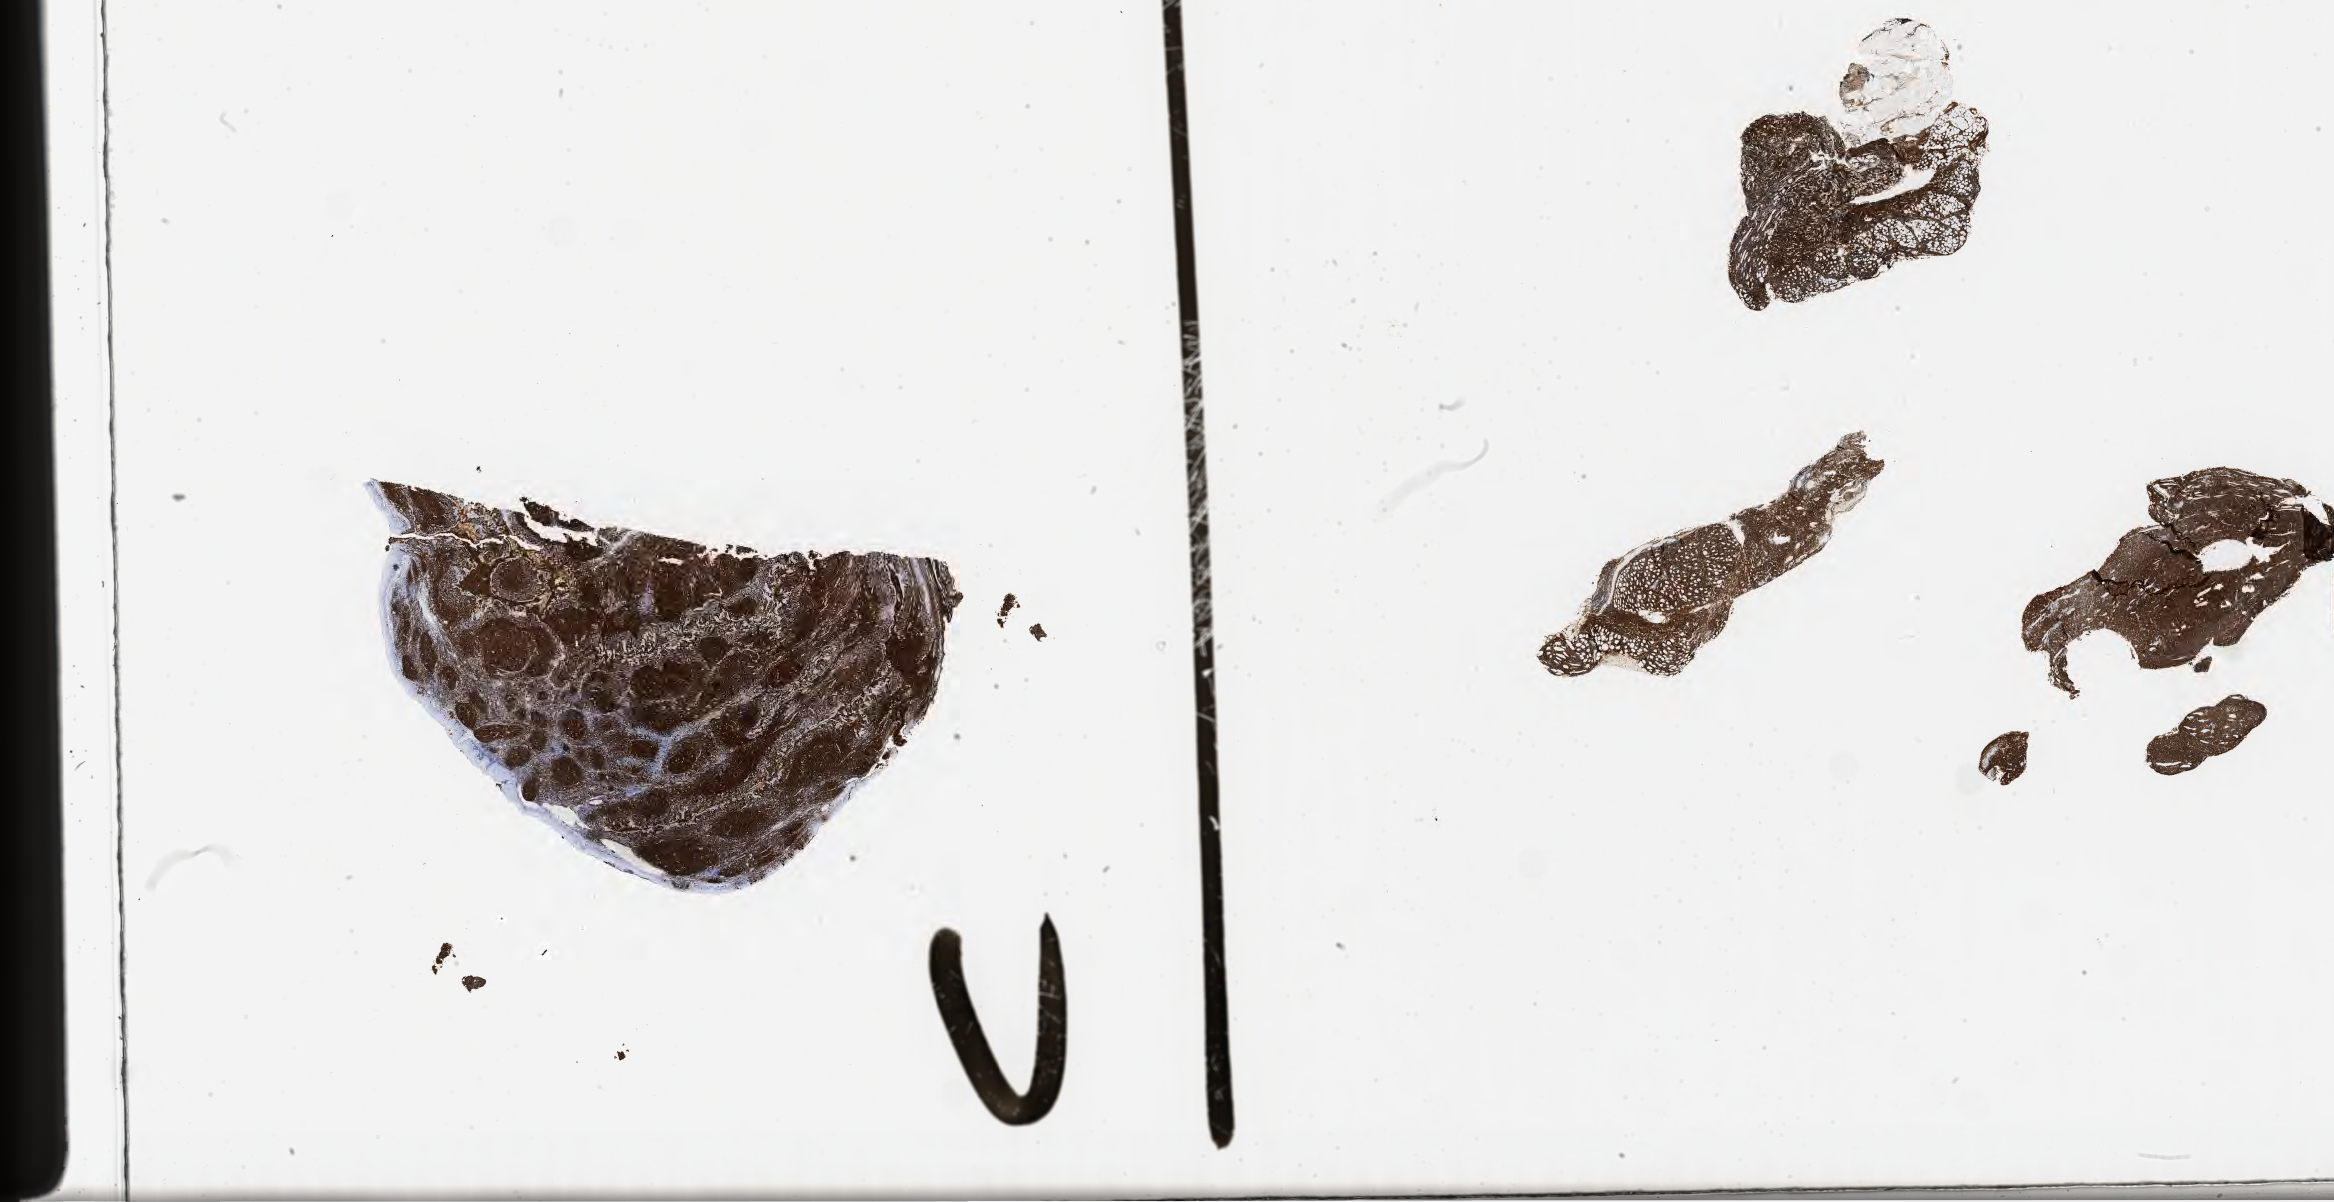
Immunohistochemistry (IHC) whole-slide image stained for CD20, whole scanned area (about 37.8 x 19.4 mm) shown as a low-resolution overview. Tumor tissue. Anatomic site: lymph node of head and neck. Patient: male, aged 55.
Diagnosis: Burkitt lymphoma, NOS.